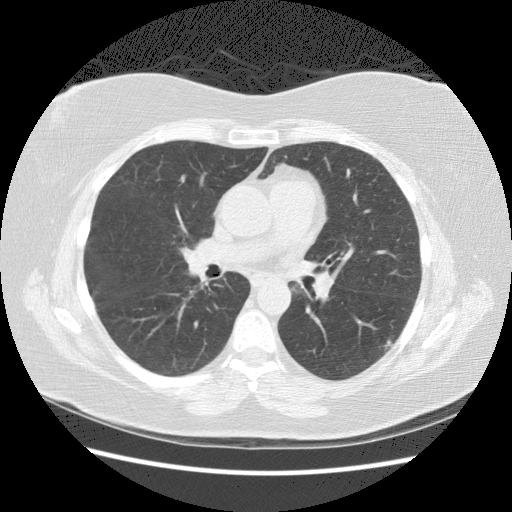
Low-dose screening chest CT, axial slice. Second annual screen. Lung window (W 1500 / L -600 HU). 2.5 mm slice thickness. Slice 76 of 140 in the series. Female participant, aged 57 years at enrolment. Current smoker at enrolment.
Expert reader's lesion annotation, bounding box <365,329,402,366> (left, top, right, bottom; pixels). The exam's reader record, not a measurement of the box and not confirmed to be the same lesion: non-calcified nodule or mass ≥4 mm, left lower lobe, 19 × 9 mm, poorly defined margins, mixed attenuation, pre-existing on the prior screen: yes; interval growth: yes. Official screen result: positive, other.